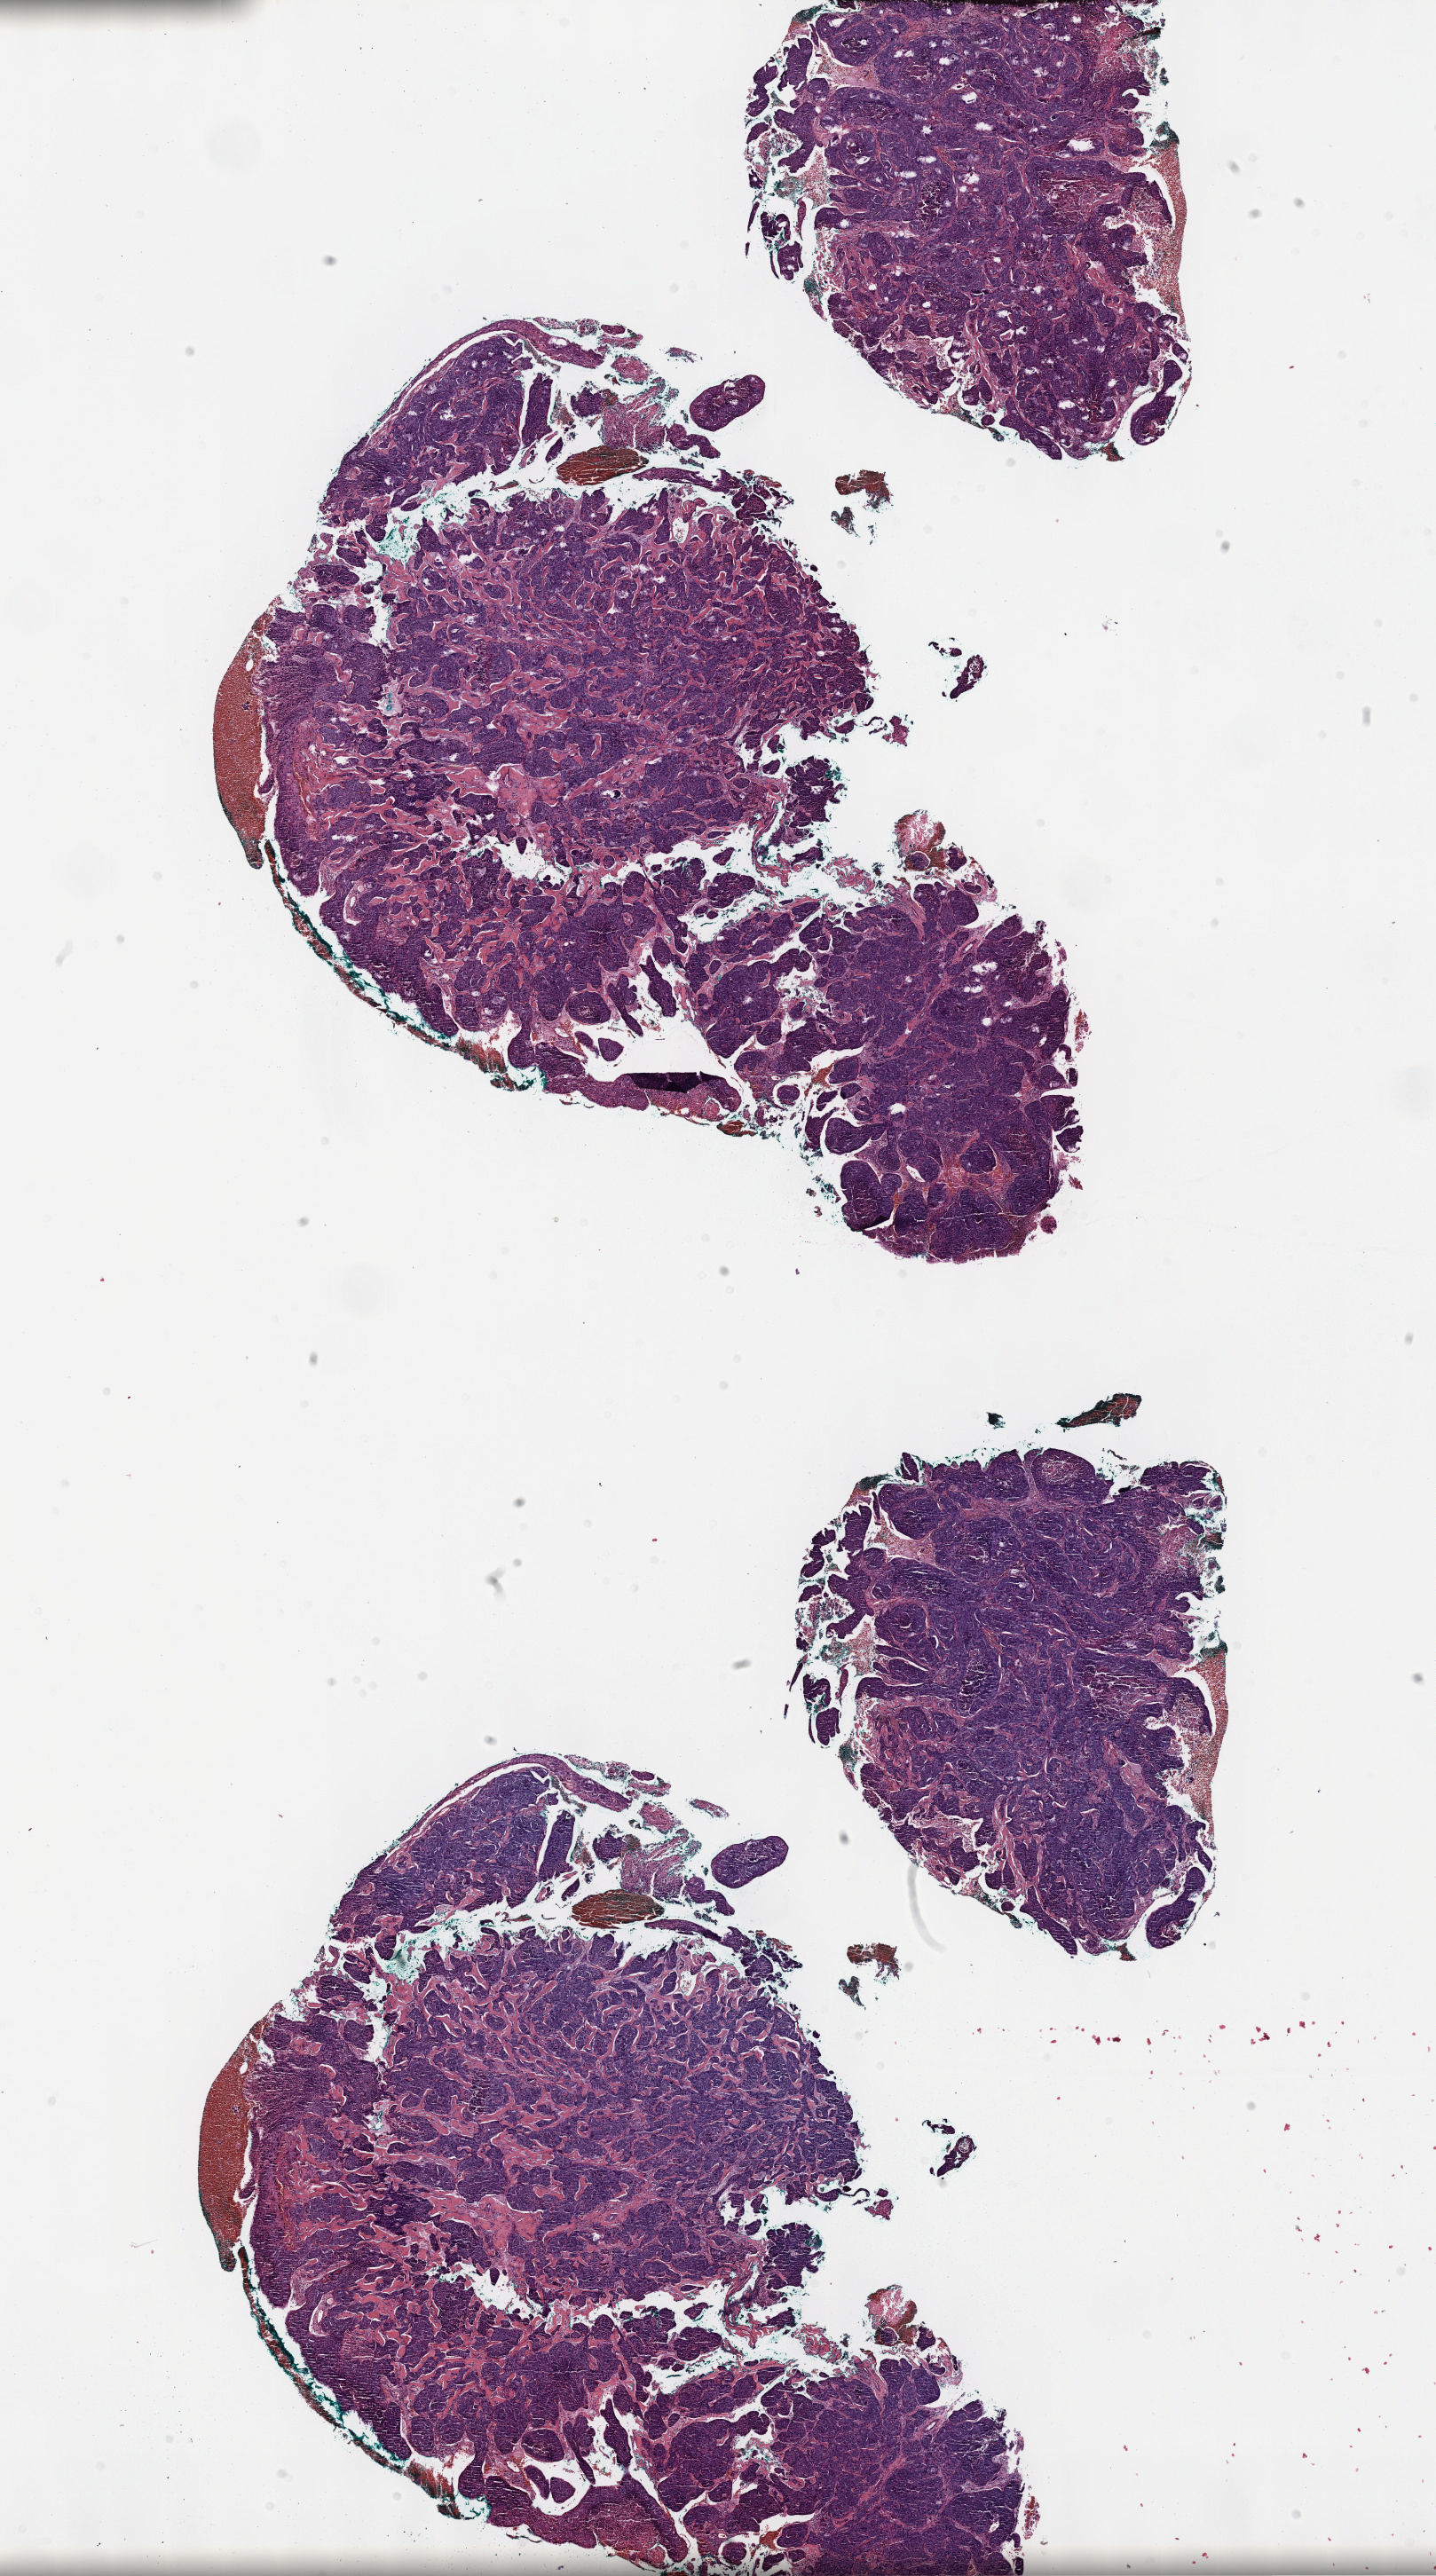
Whole-slide histology image, Hematoxylin and eosin (H&E) stained — whole scanned area (about 13.1 x 23.5 mm) shown as a low-resolution overview, formalin-fixed paraffin-embedded (FFPE) diagnostic section, primary tumour sample from the cervix. Female, age 67 years at initial diagnosis. Histologic grade: G2 (moderately differentiated).
• FIGO stage: IIIB
• diagnosis: Squamous cell carcinoma, NOS (cervix uteri)